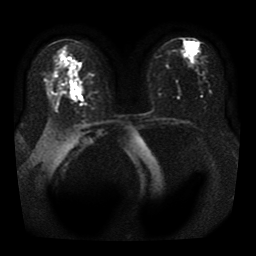
Breast MRI, one axial slice; position 19 of 41 along the scan axis; diffusion-weighted series; image 2 of 4 stored at this slice position (different b-values; order by instance number); 1.5 T; 5 mm slice thickness; 256 × 256 image matrix. Female patient.
Annotated regions visible in this slice (manually delineated by an expert):
- tumour on diffusion-weighted imaging: bounding box [x1, y1, x2, y2] px = [71, 81, 83, 97]